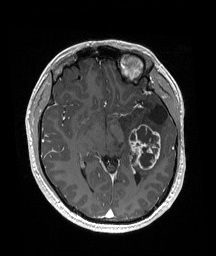
Brain MRI from a brain-tumour surgery series, one axial slice; T1-weighted post-contrast; 1 mm slice thickness; 216 × 256 image matrix. From the clinical record (not read from this slice): histopathology: Glioneuronal tumor; WHO grade: 2; tumour location: Left Superior Temporal Gyrus.
Annotated regions visible in this slice (expert manual segmentation):
- previous resection cavity: bounding box [x1, y1, x2, y2] px = [151, 105, 168, 124]
- tumour: [129, 124, 161, 170]